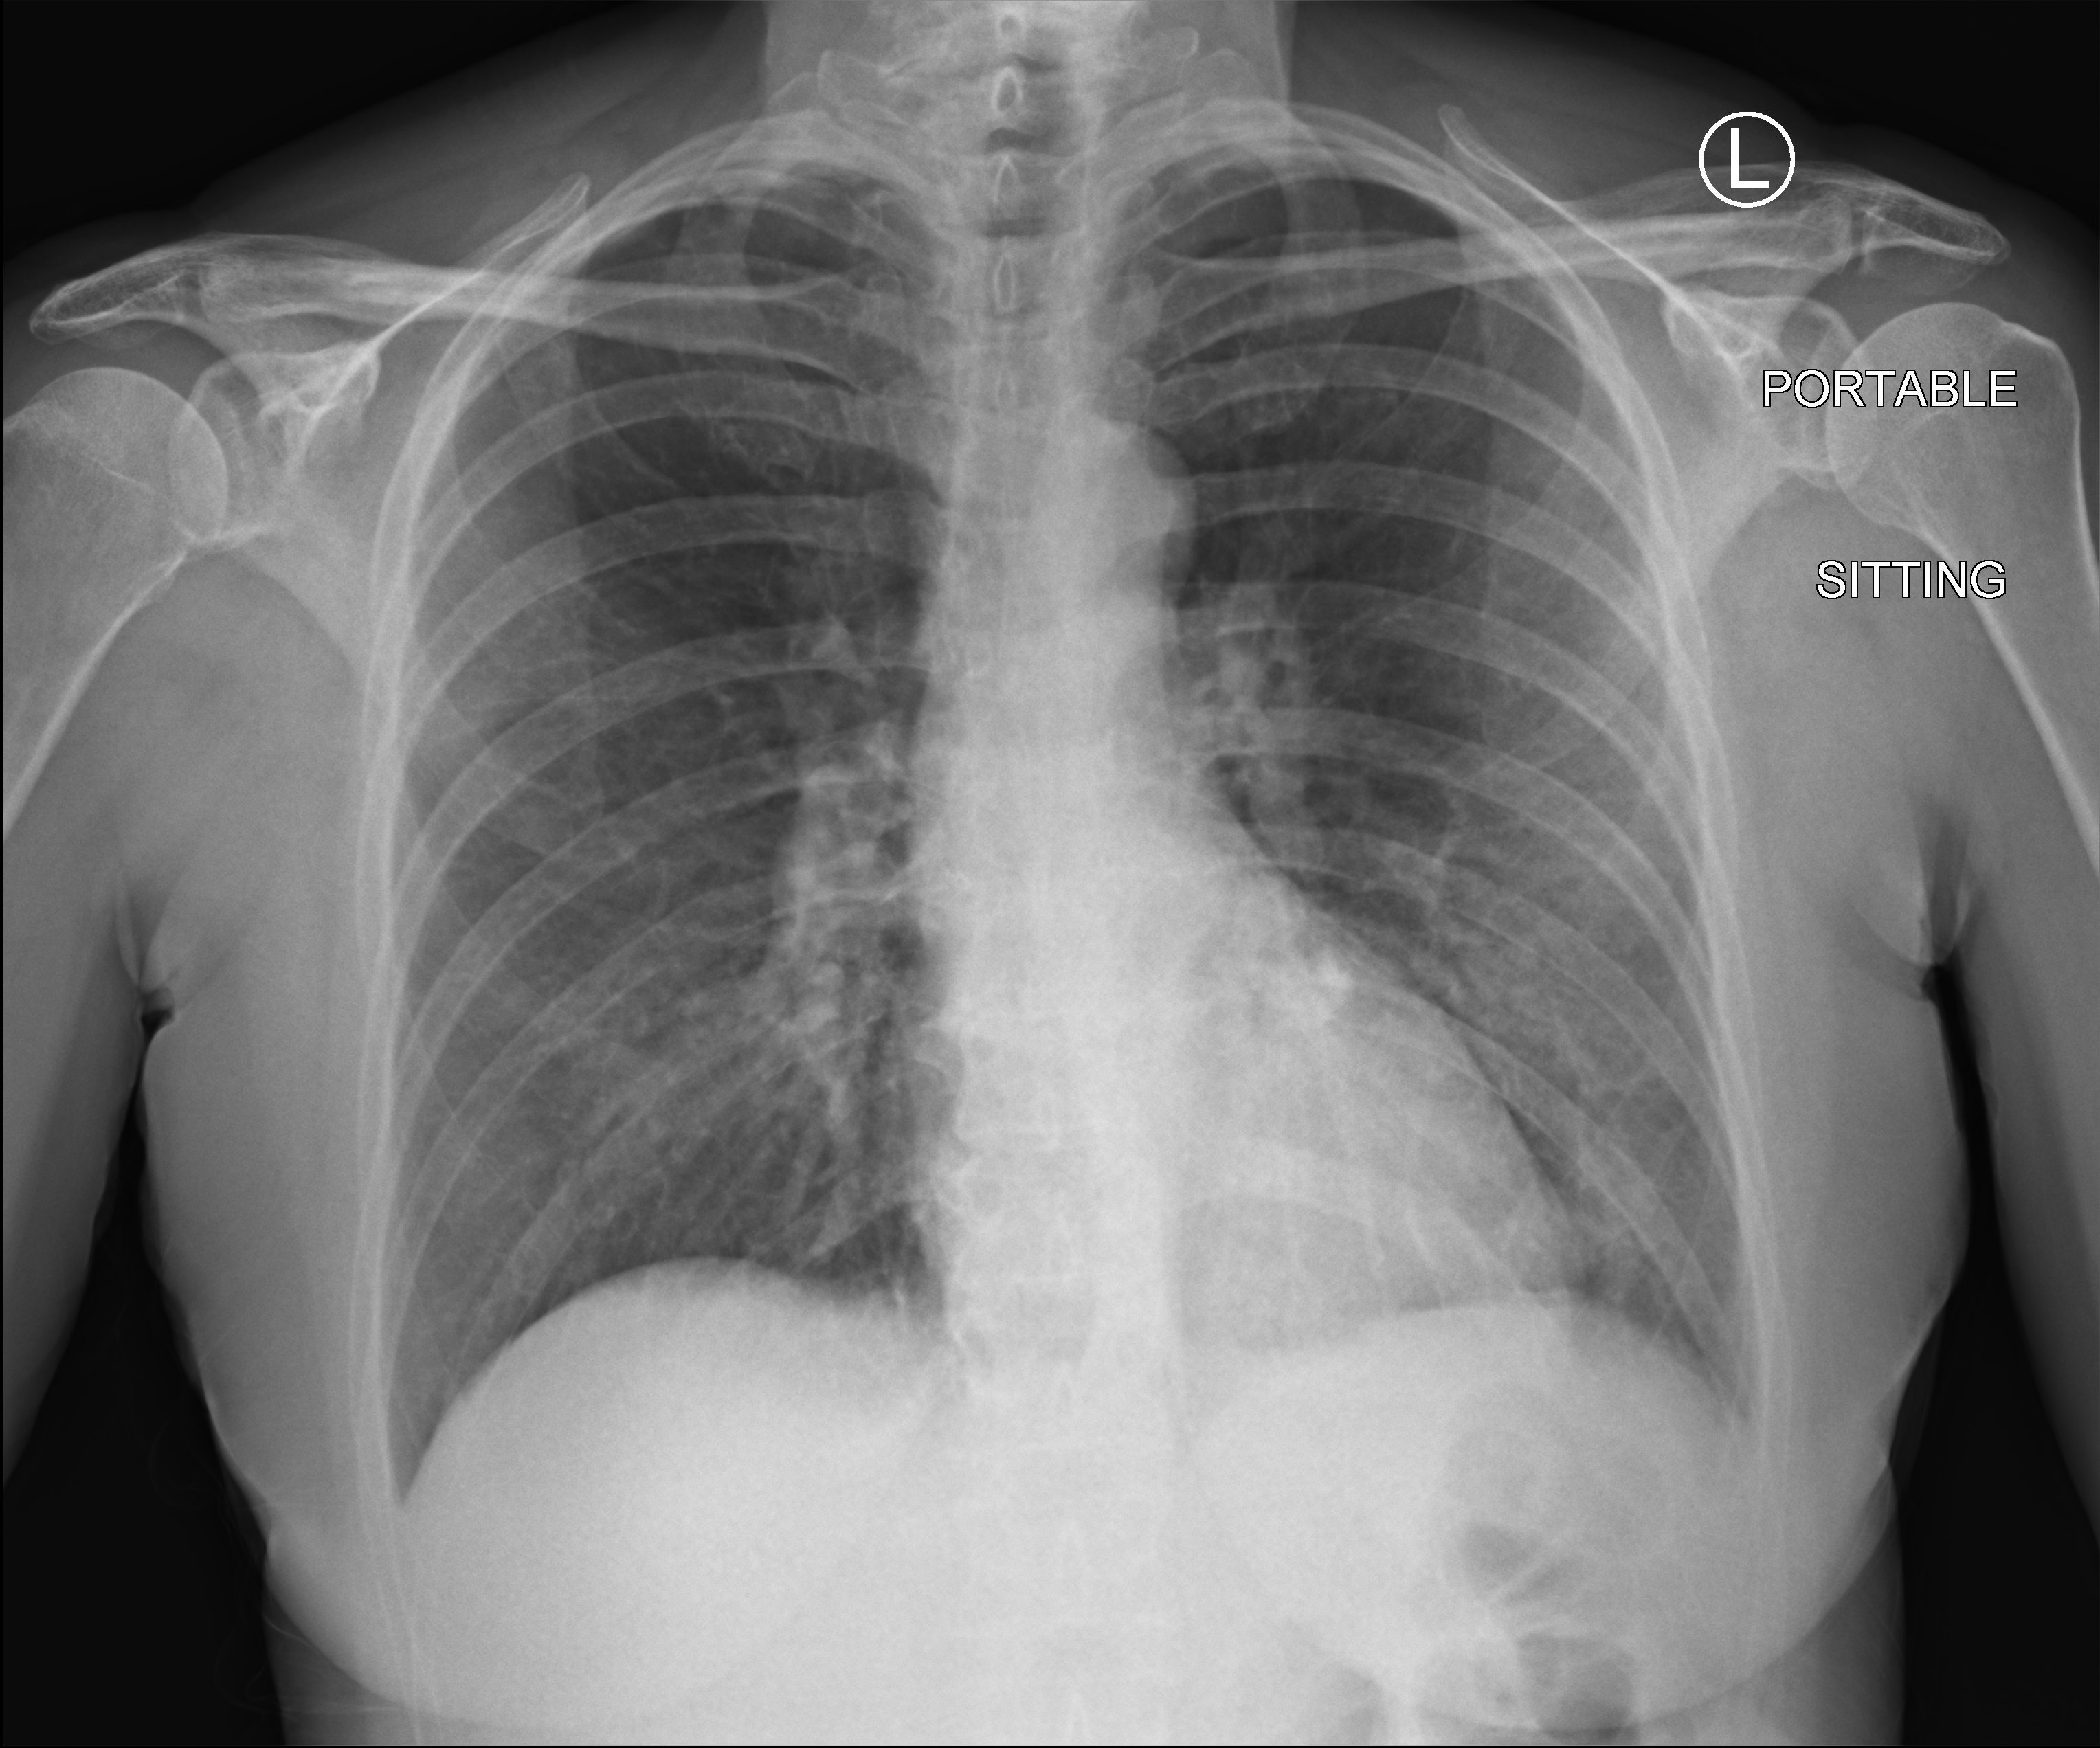
Chest X-ray (portable), anteroposterior (AP) projection. Female patient hospitalised with COVID-19, age 60–74 years.
Hospital-stay facts (about this admission, not read from this image; timing relative to this image not recorded):
- mechanically ventilated during this hospital stay: no
- length of hospital stay: 10 days
- admitted to intensive care during this hospital stay: no